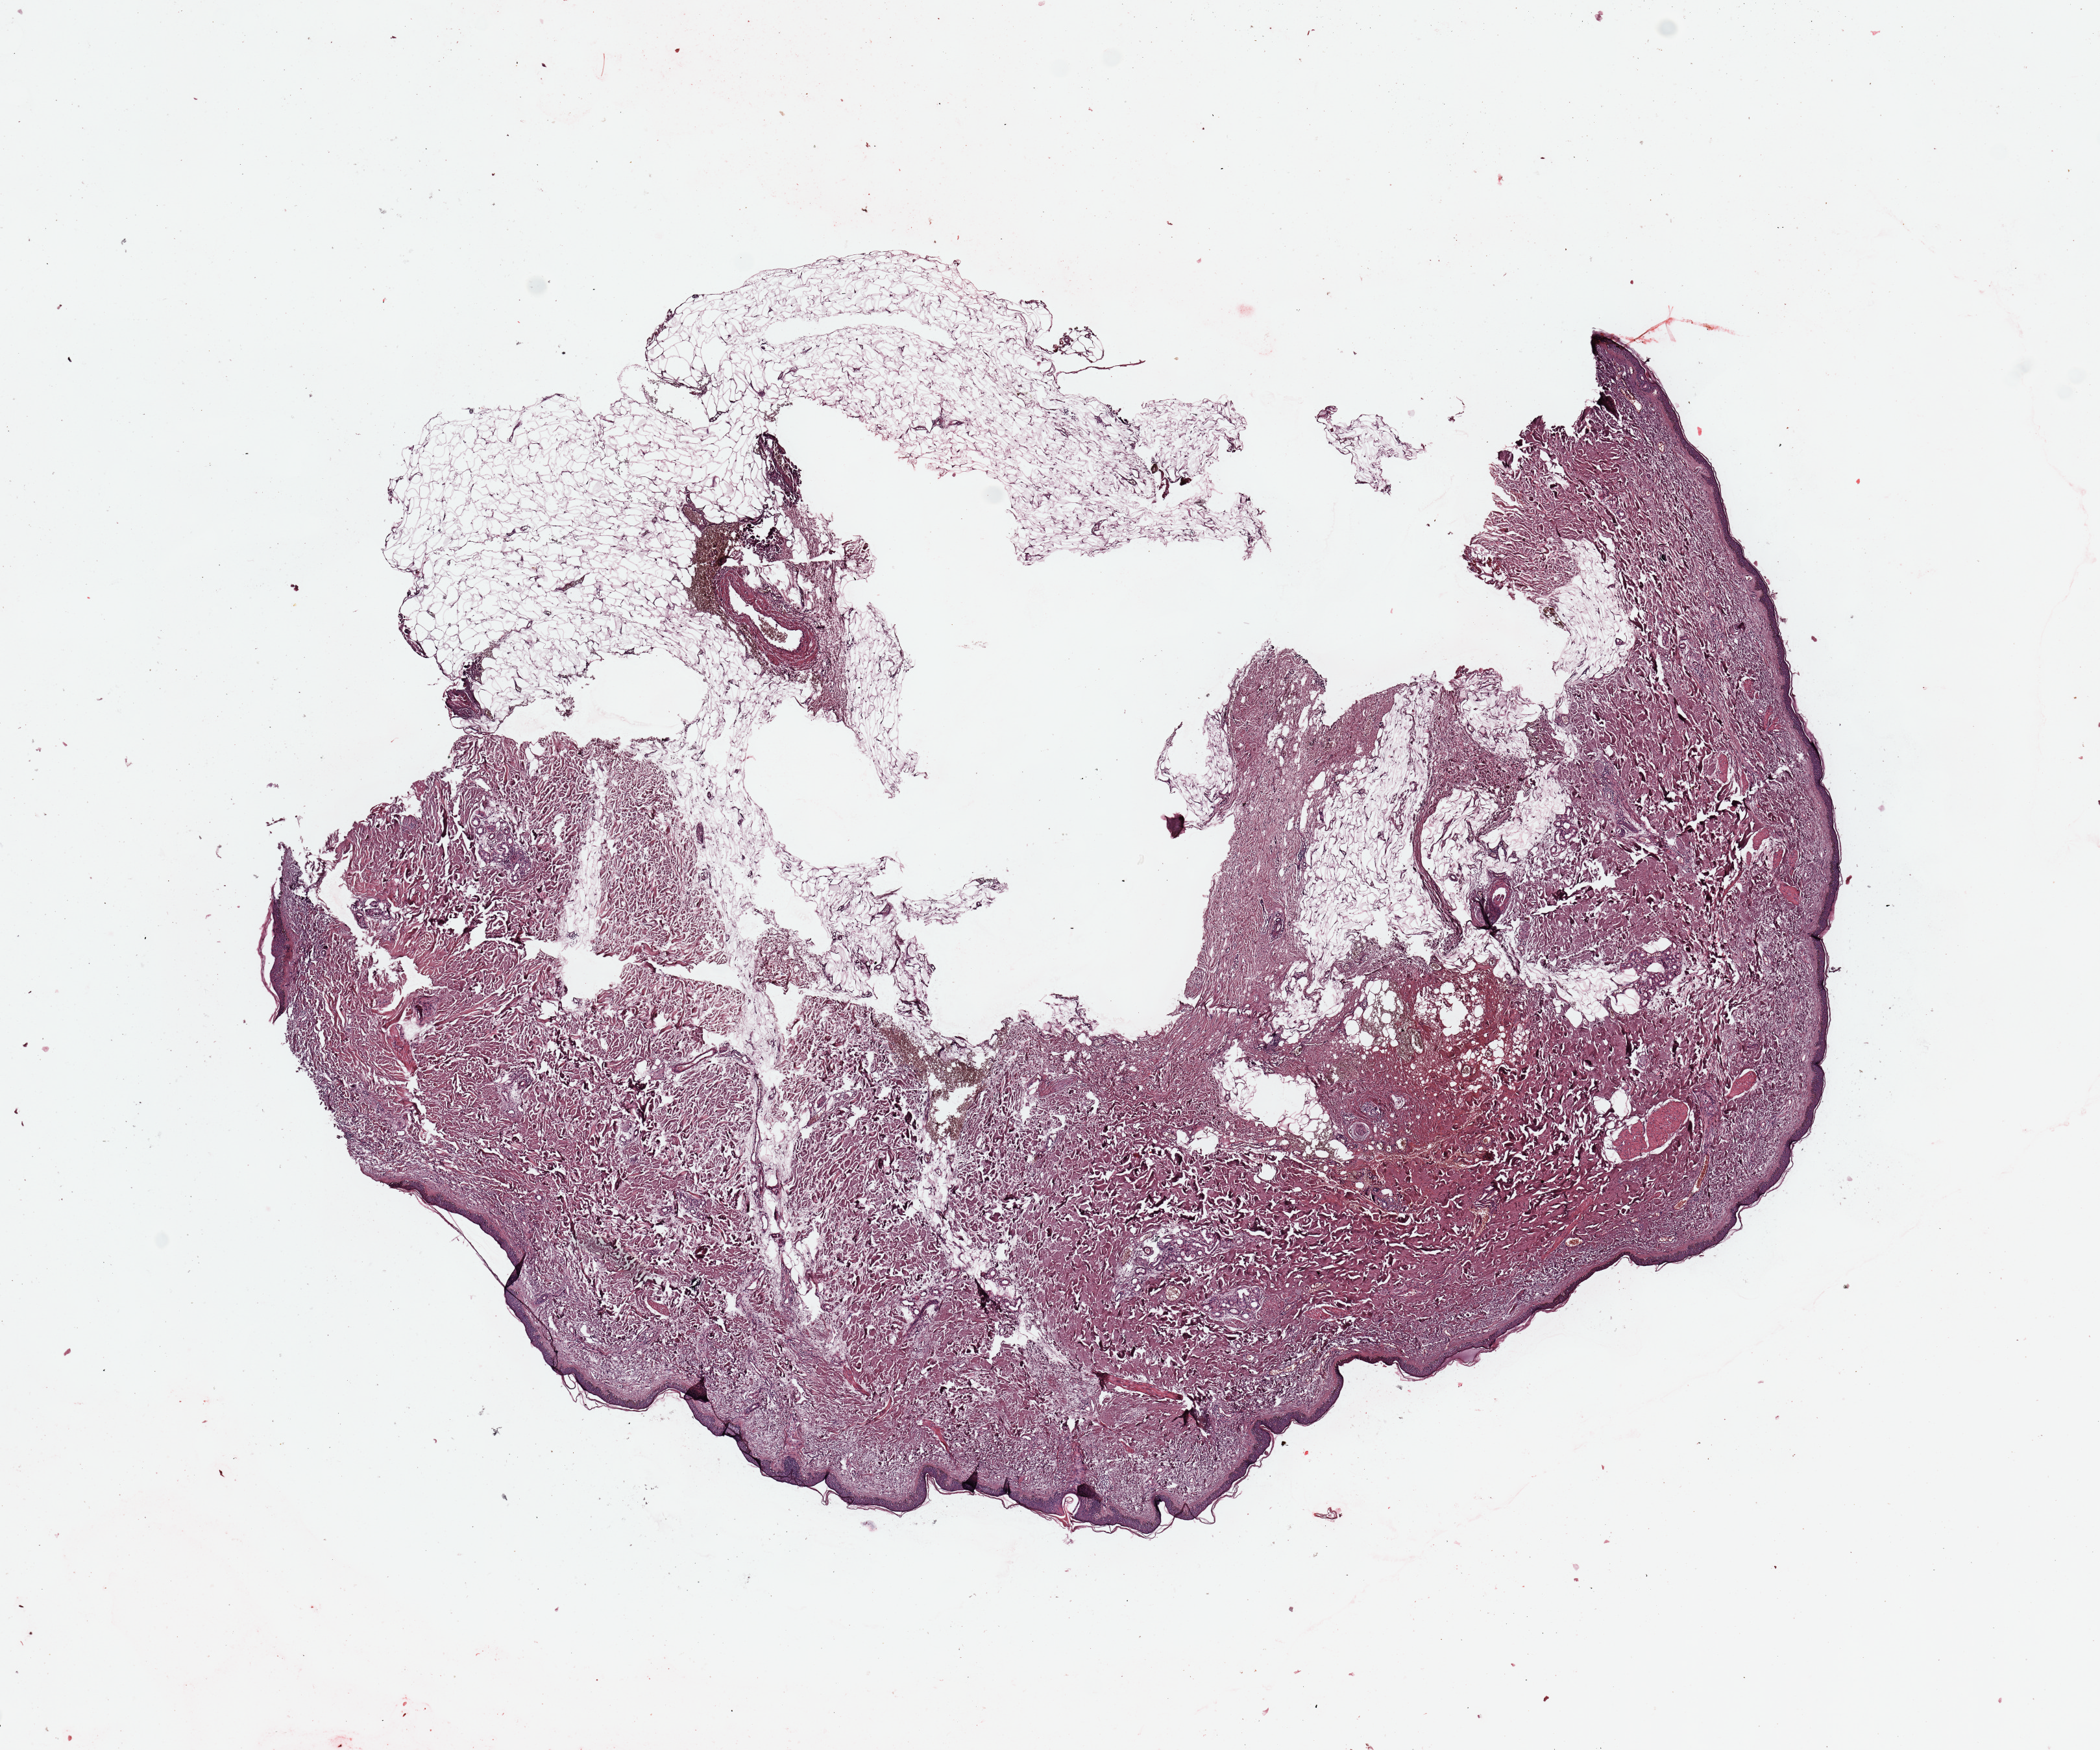
H&E whole-slide image — a low-resolution overview of the entire scanned area, about 12.8 x 10.7 mm; normal (non-tumour) tissue sample. Male, 72 y/o.
This section: normal (non-tumour) tissue from the same patient. Patient diagnosis (cohort enrolment): sarcoma (site not recorded at cohort level).